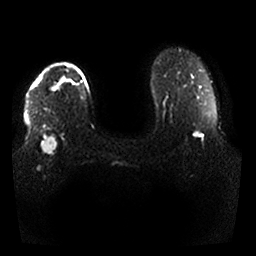
Breast MRI, one axial slice. Position 24 of 25 along the scan axis. Diffusion-weighted series; image 2 of 4 stored at this slice position (different b-values; order by instance number). 1.5 T. 4 mm slice thickness. 256 × 256 image matrix. Female patient.
Annotated regions visible in this slice (expert manual segmentation):
- tumour on diffusion-weighted imaging: bounding box <41,87,57,154> (left, top, right, bottom; pixels)